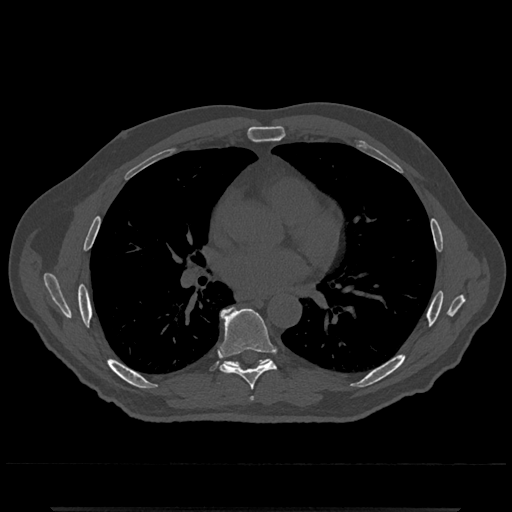
CT including the spine, one axial slice. Position 711 of 797 along the scan axis. 120 kVp. Bone window (W 1800 / L 400 HU). 0.5 mm slice thickness. 512 × 512 image matrix, field of view 393 × 393 mm. Patient: male, 67 years. Case-level facts recorded for this patient, not image findings: primary cancer: prostate.
Annotated regions visible in this slice (semi-automatic segmentation, software-assisted and operator-edited):
- T7 vertebra: box from (x=219, y=308) to (x=277, y=390) px
- T8 vertebra: (x=220, y=307)–(x=270, y=367)